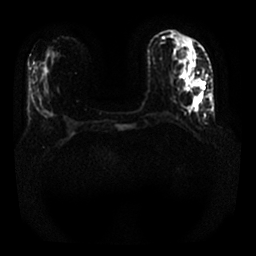
Breast MRI, one axial slice. Diffusion-weighted series; image 2 of 4 stored at this slice position (different b-values; order by instance number). 1.5 T. 256 × 256 image matrix. Female patient.
Annotated regions visible in this slice (manually delineated by an expert):
- tumour on diffusion-weighted imaging: box from (x=193, y=91) to (x=202, y=104) px